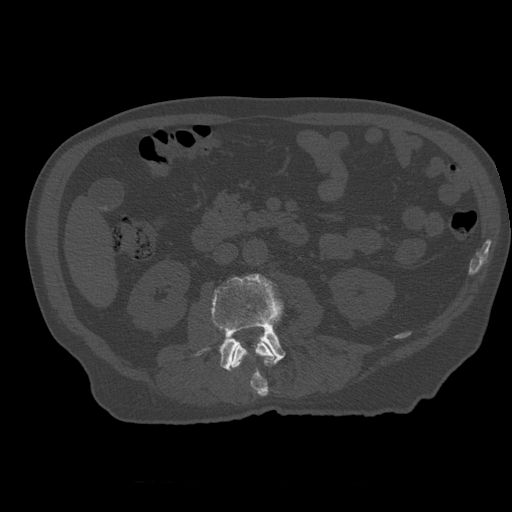
CT including the spine, one axial slice; slice 198 of 399 in the series (ordered by position); reconstruction kernel STANDARD; bone window (W 1800 / L 400 HU); 1.25 mm slice thickness; 512 × 512 image matrix. Patient age 73 years. From the clinical record (not read from this slice): primary cancer: prostate; vertebrae with lytic lesions (as recorded): L2.
Outlined on this slice (semi-automatic segmentation, software-assisted and operator-edited):
- L2 vertebra: box from (x=230, y=341) to (x=275, y=397) px
- L3 vertebra: (x=197, y=274)–(x=286, y=371)